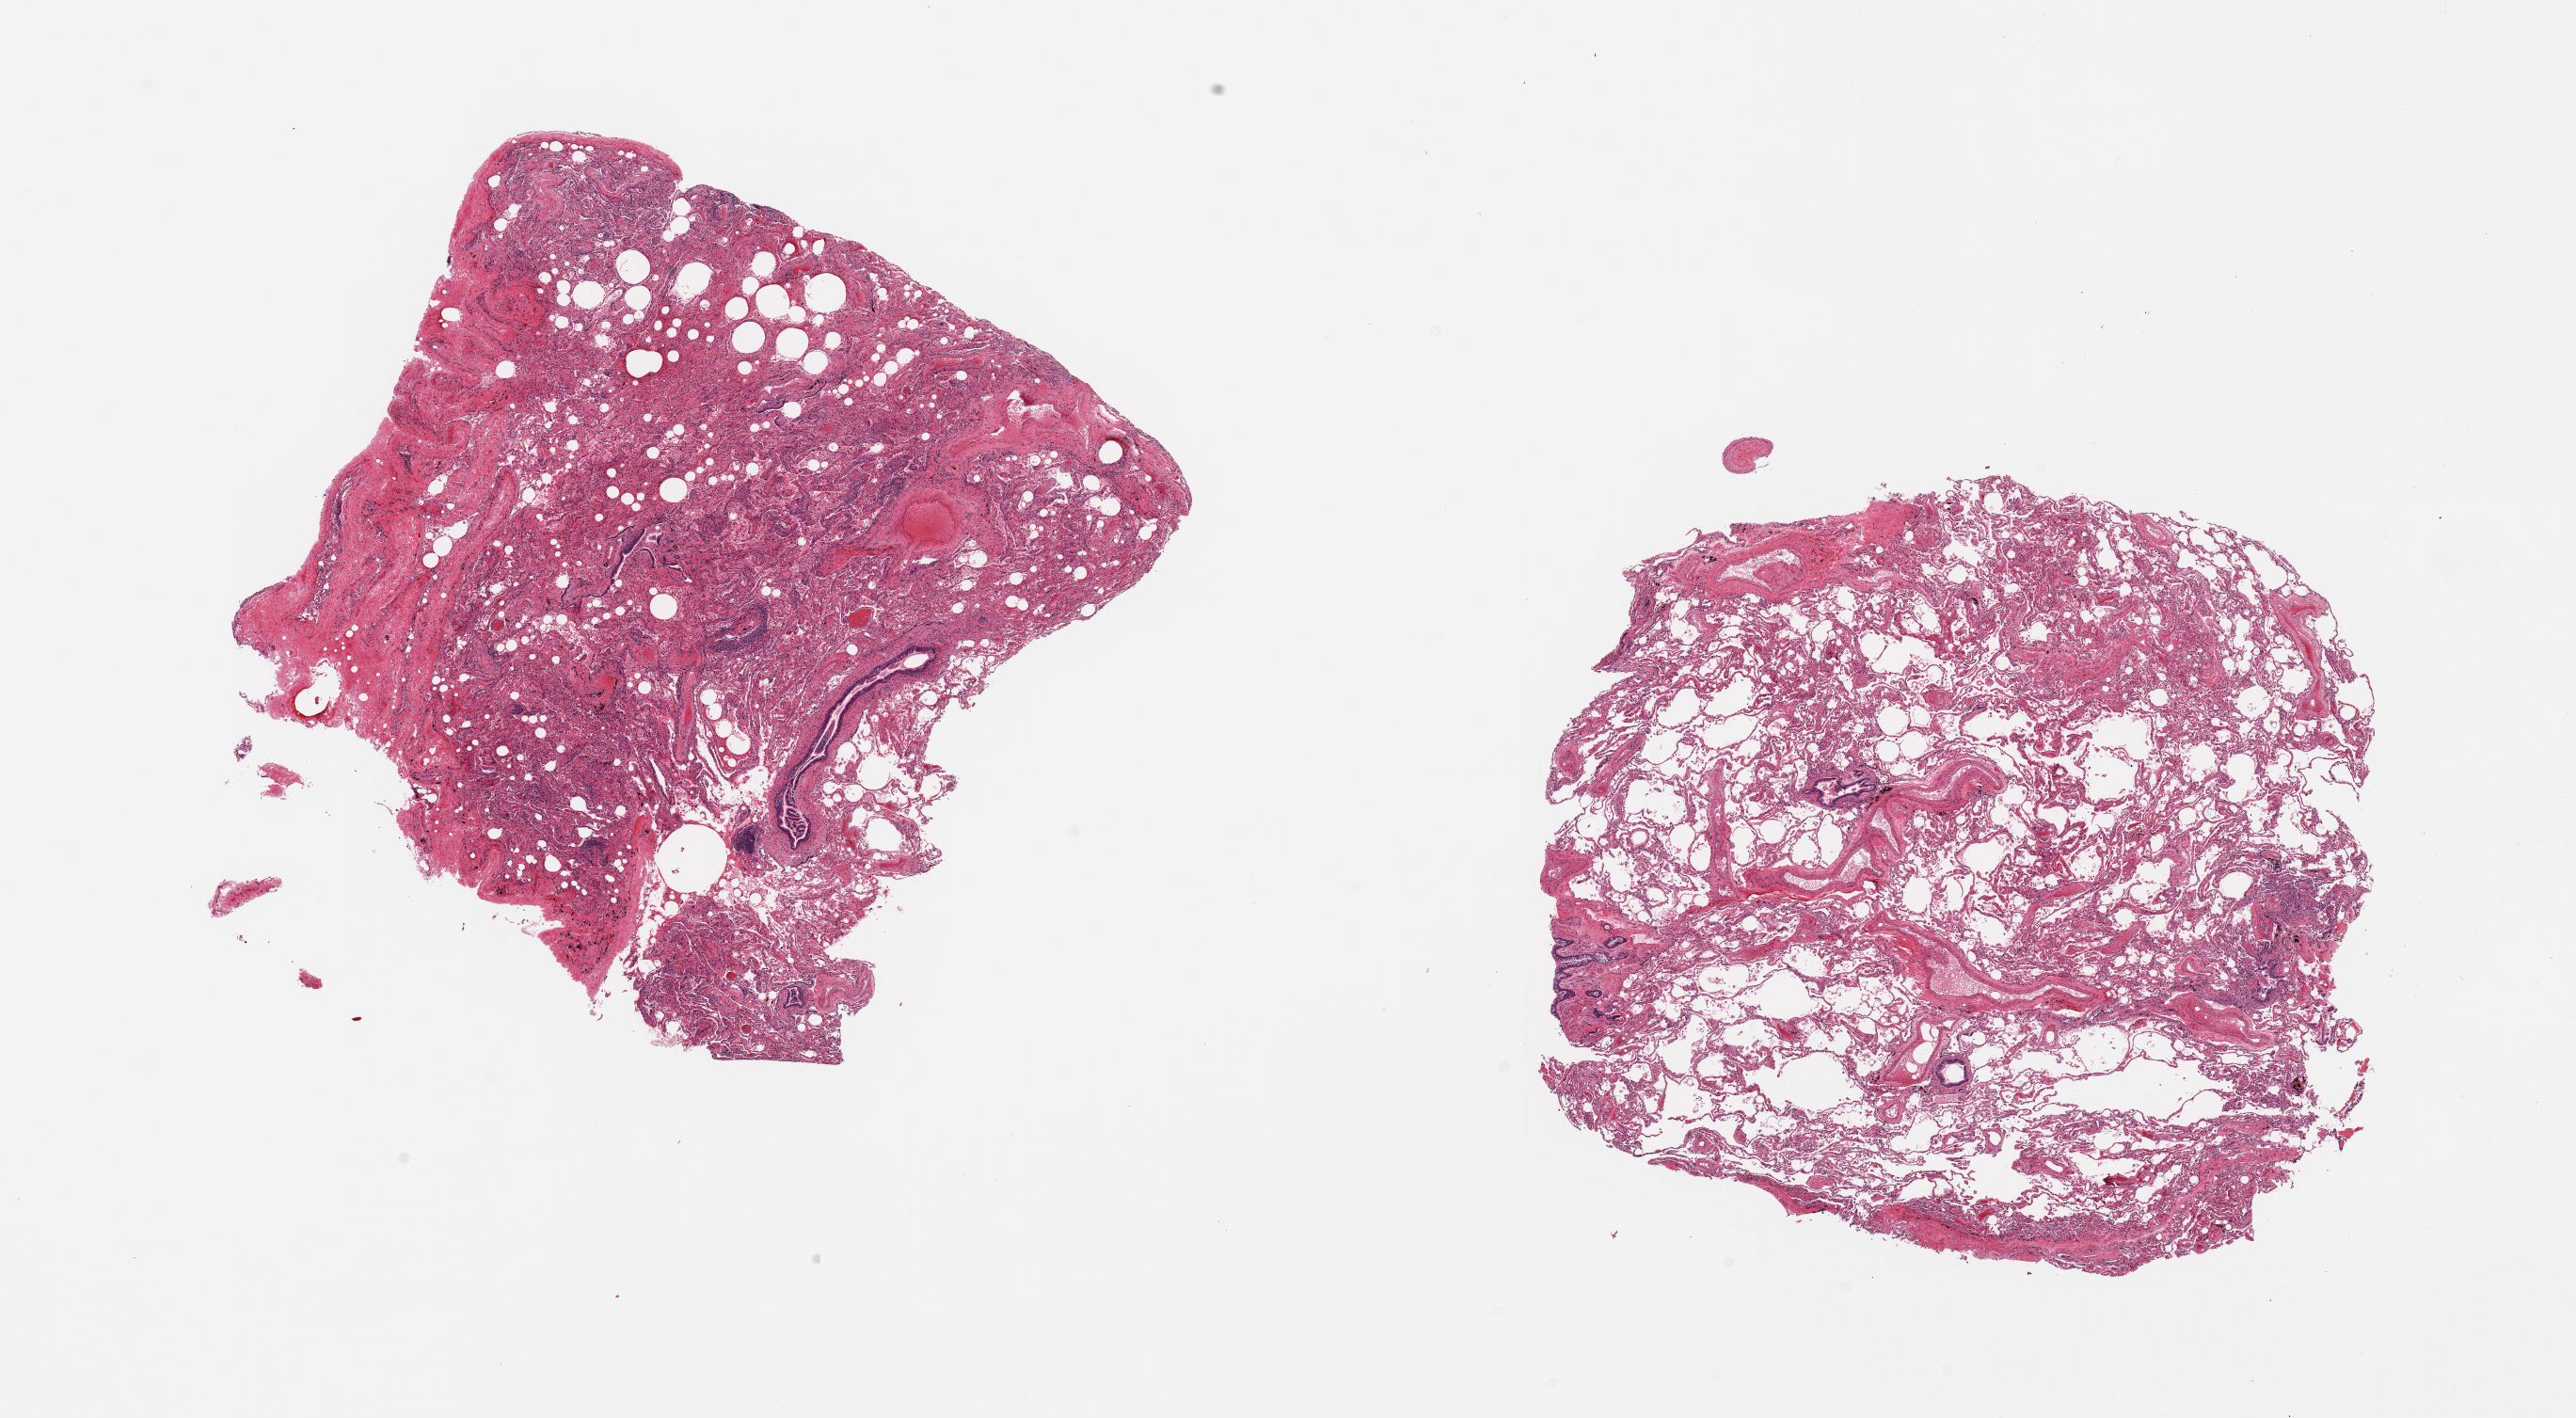
Digitized H&E-stained section, low-resolution overview of the scanned area, about 21.7 x 11.9 mm, PAXgene-fixed, paraffin-embedded tissue, target tissue: lung, tissue donor sample.
Reviewer comment on this tissue sample: 2 pieces; emphysema in 1 piece; alveolar hemorrhage, atelectasis and fibrosis in other.